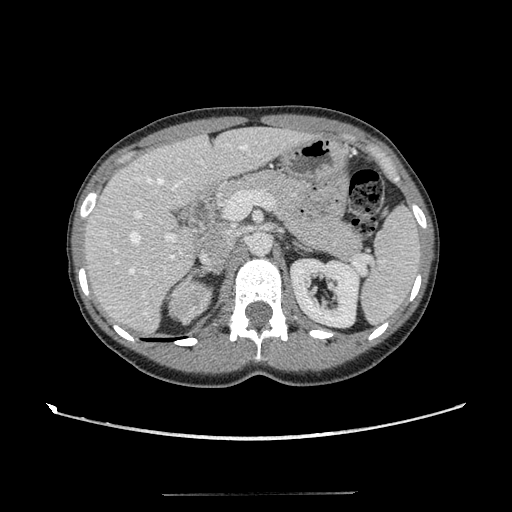
Contrast-enhanced abdominal CT, one axial slice. Position 71 of 117 along the scan axis. Intravenous contrast given. Soft-tissue window (W 400 / L 40 HU). 2.5 mm slice thickness. 512 × 512 image matrix. Female patient, age 35 years. From the clinical record (not read from this slice): diagnosis: adrenocortical carcinoma; tumour side: right adrenal; tumour size at pathology: 3 cm; Ki-67 index: 21 %; stage (as recorded): 3.
Annotated regions visible in this slice (semi-automatic segmentation, software-assisted and operator-edited):
- mass: bounding box (x1, y1, x2, y2) in pixels: (170, 283, 209, 324)